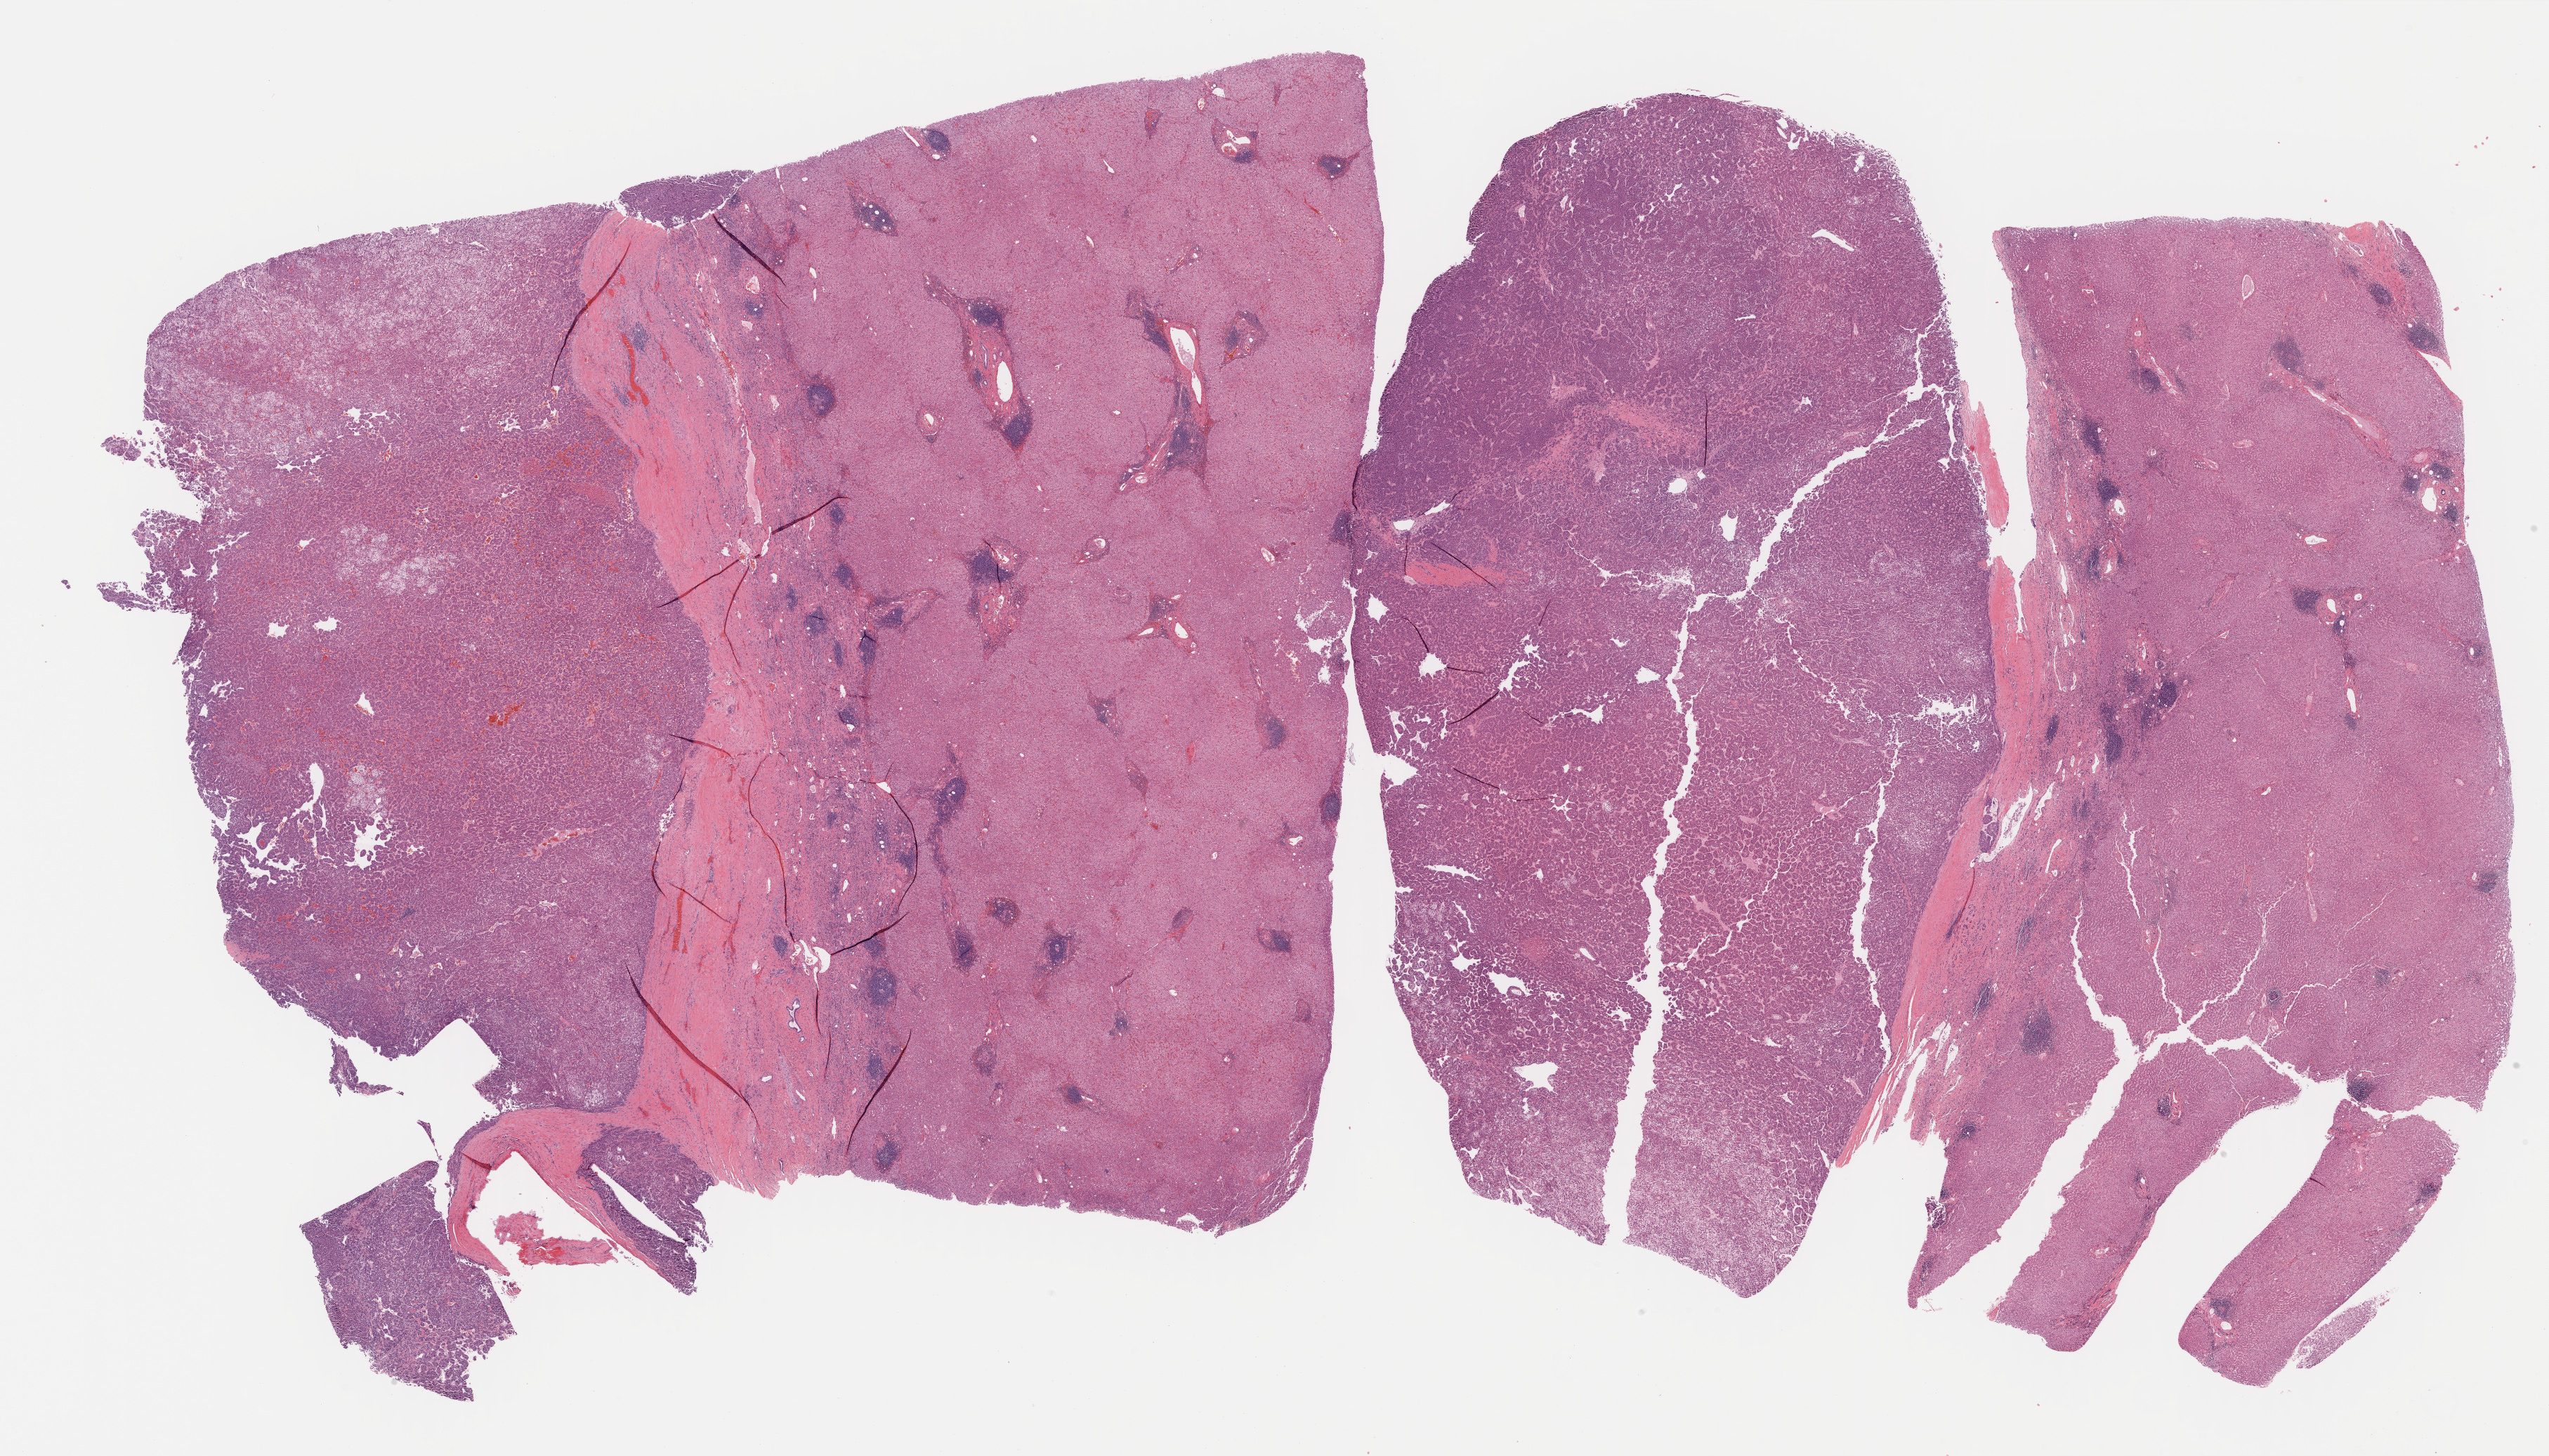
Whole-slide histology image, Hematoxylin and eosin (H&E) stained, a low-resolution overview of the entire scanned area, about 29.4 x 16.8 mm (slide scanned at 40x), FFPE section, sample: primary tumour, liver. Patient: female, age at initial diagnosis 57 years. Histologic grade: G2 (moderately differentiated).
- diagnosis: Hepatocellular carcinoma, NOS
- AJCC pathologic stage: I (6th edition)